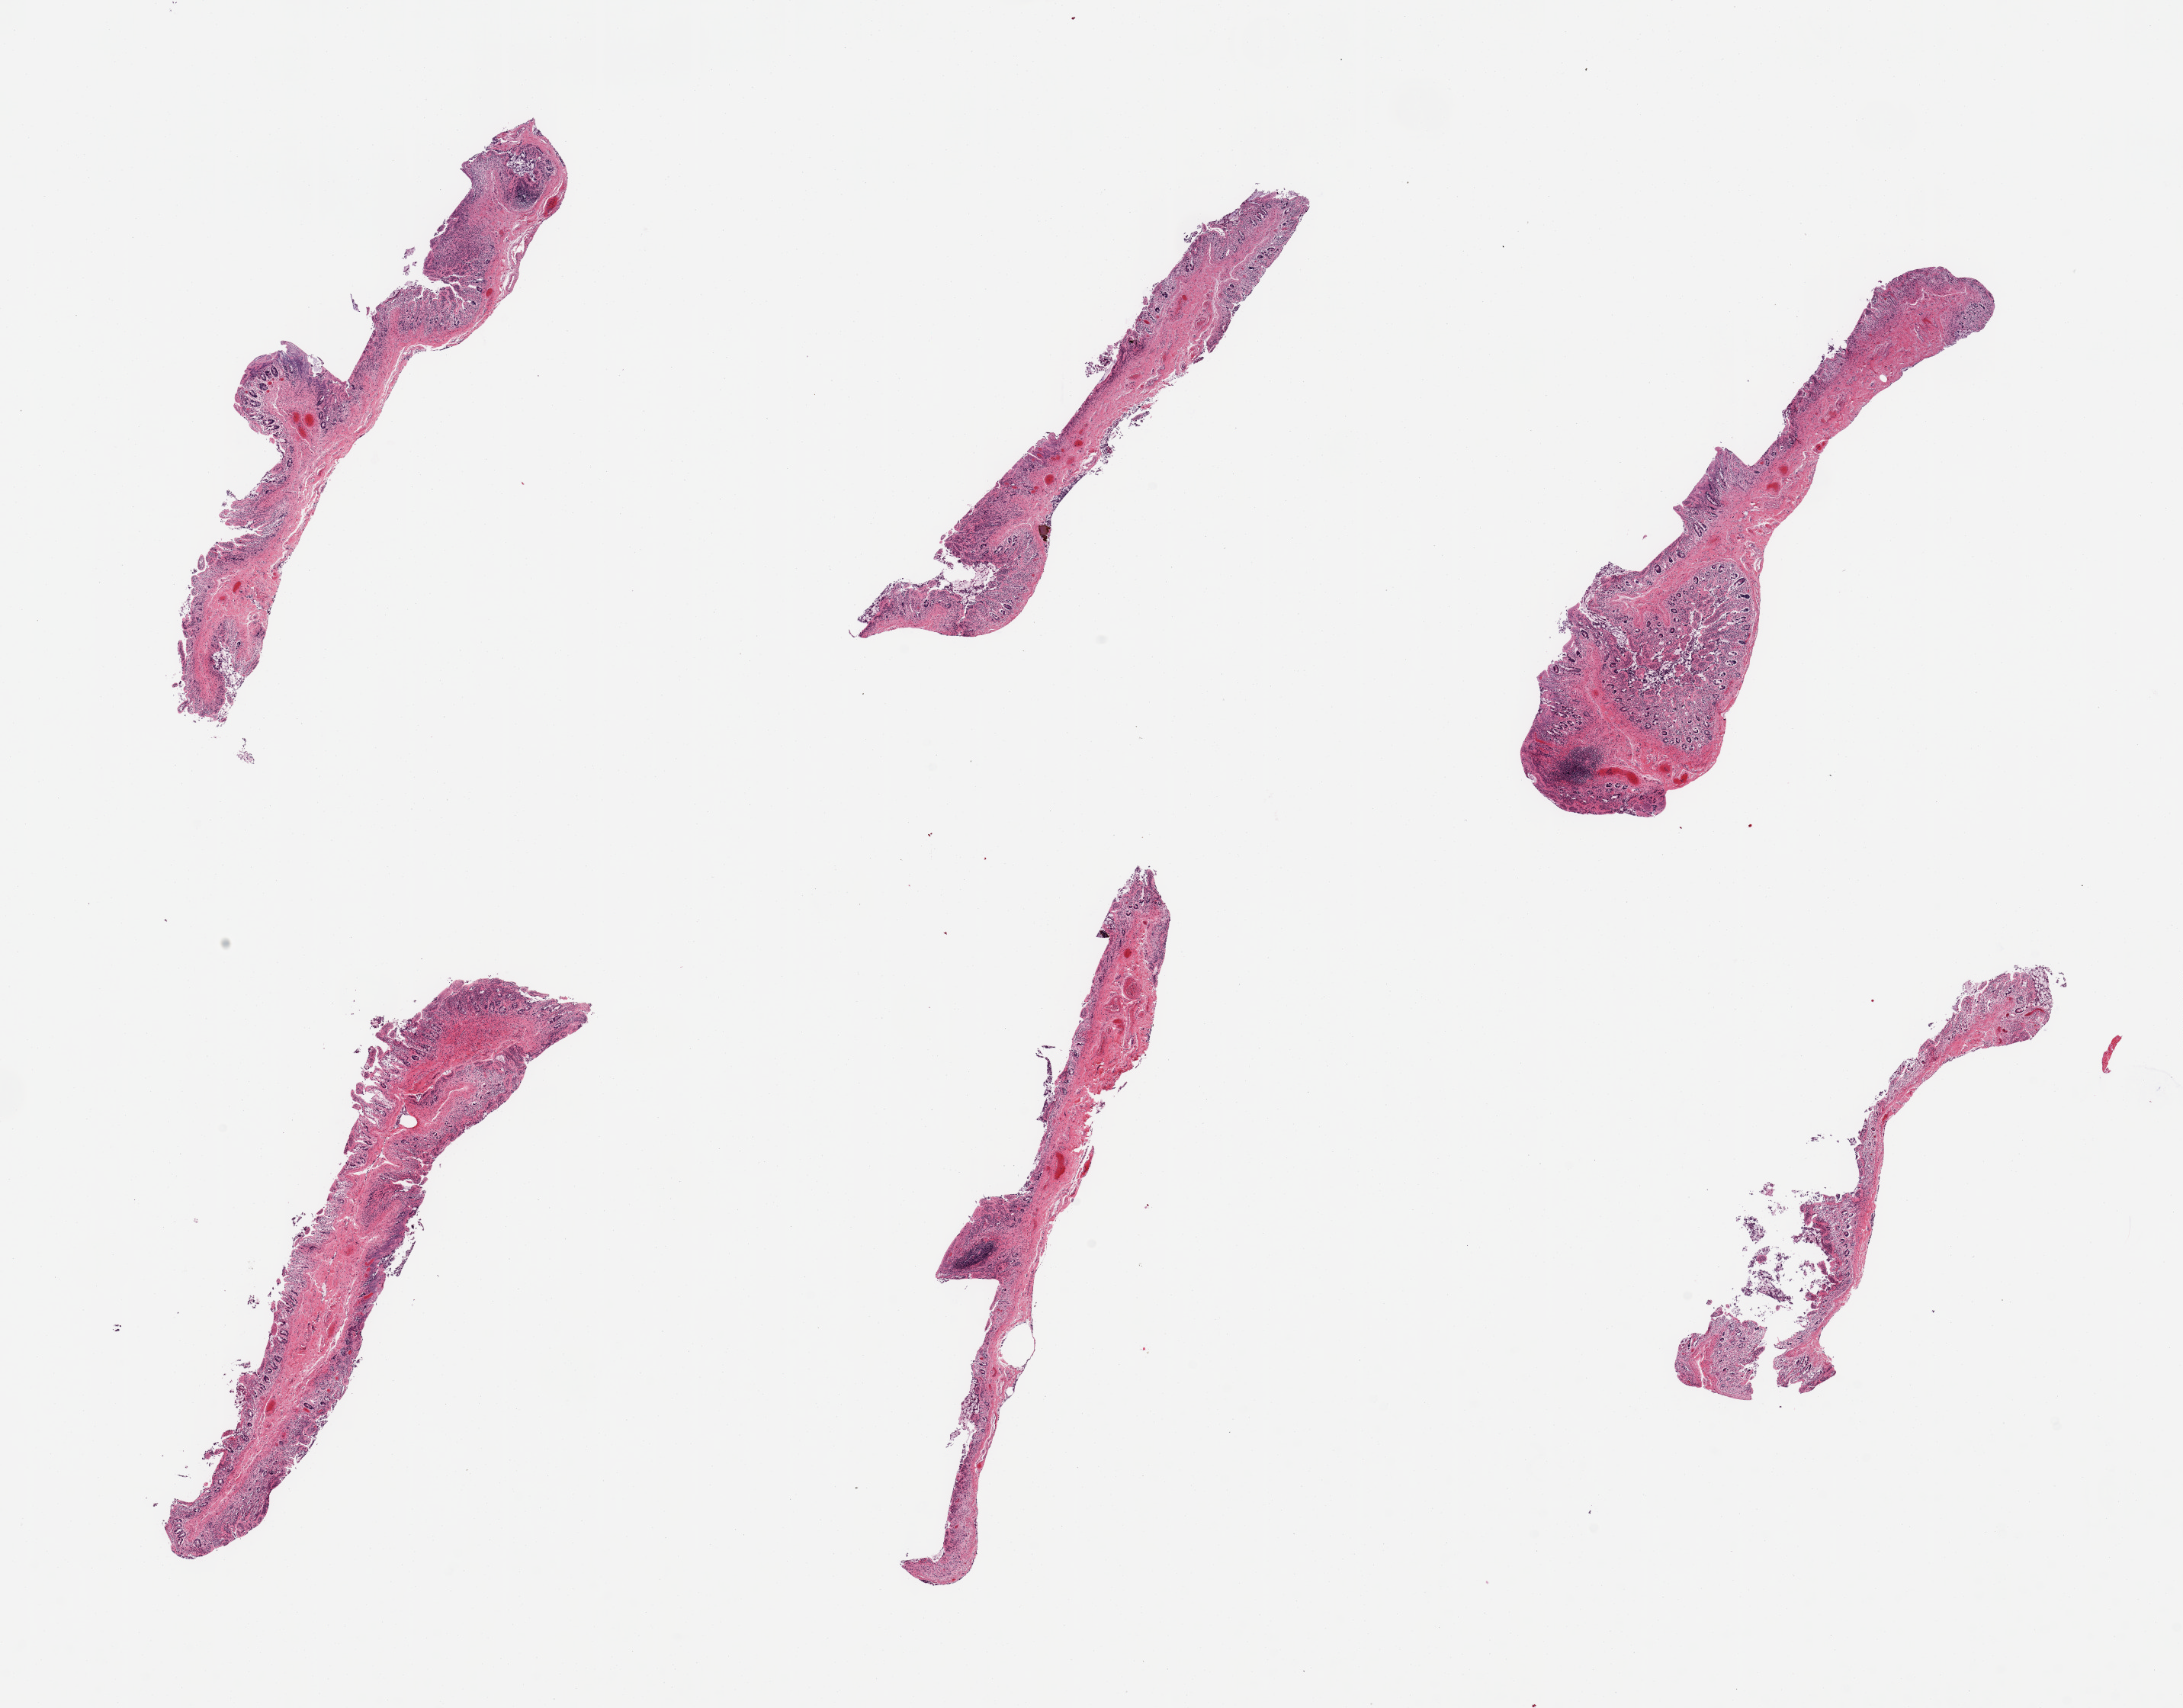
Digitized H&E-stained section, brightfield, a low-resolution overview of the entire scanned area, about 22.6 x 17.7 mm. PAXgene-fixed paraffin-embedded (PFPE) section. Section of ileum (target tissue). Tissue donor sample.
Pathologist's review note for this sample: 6 pieces, no target lymphoid aggregates.